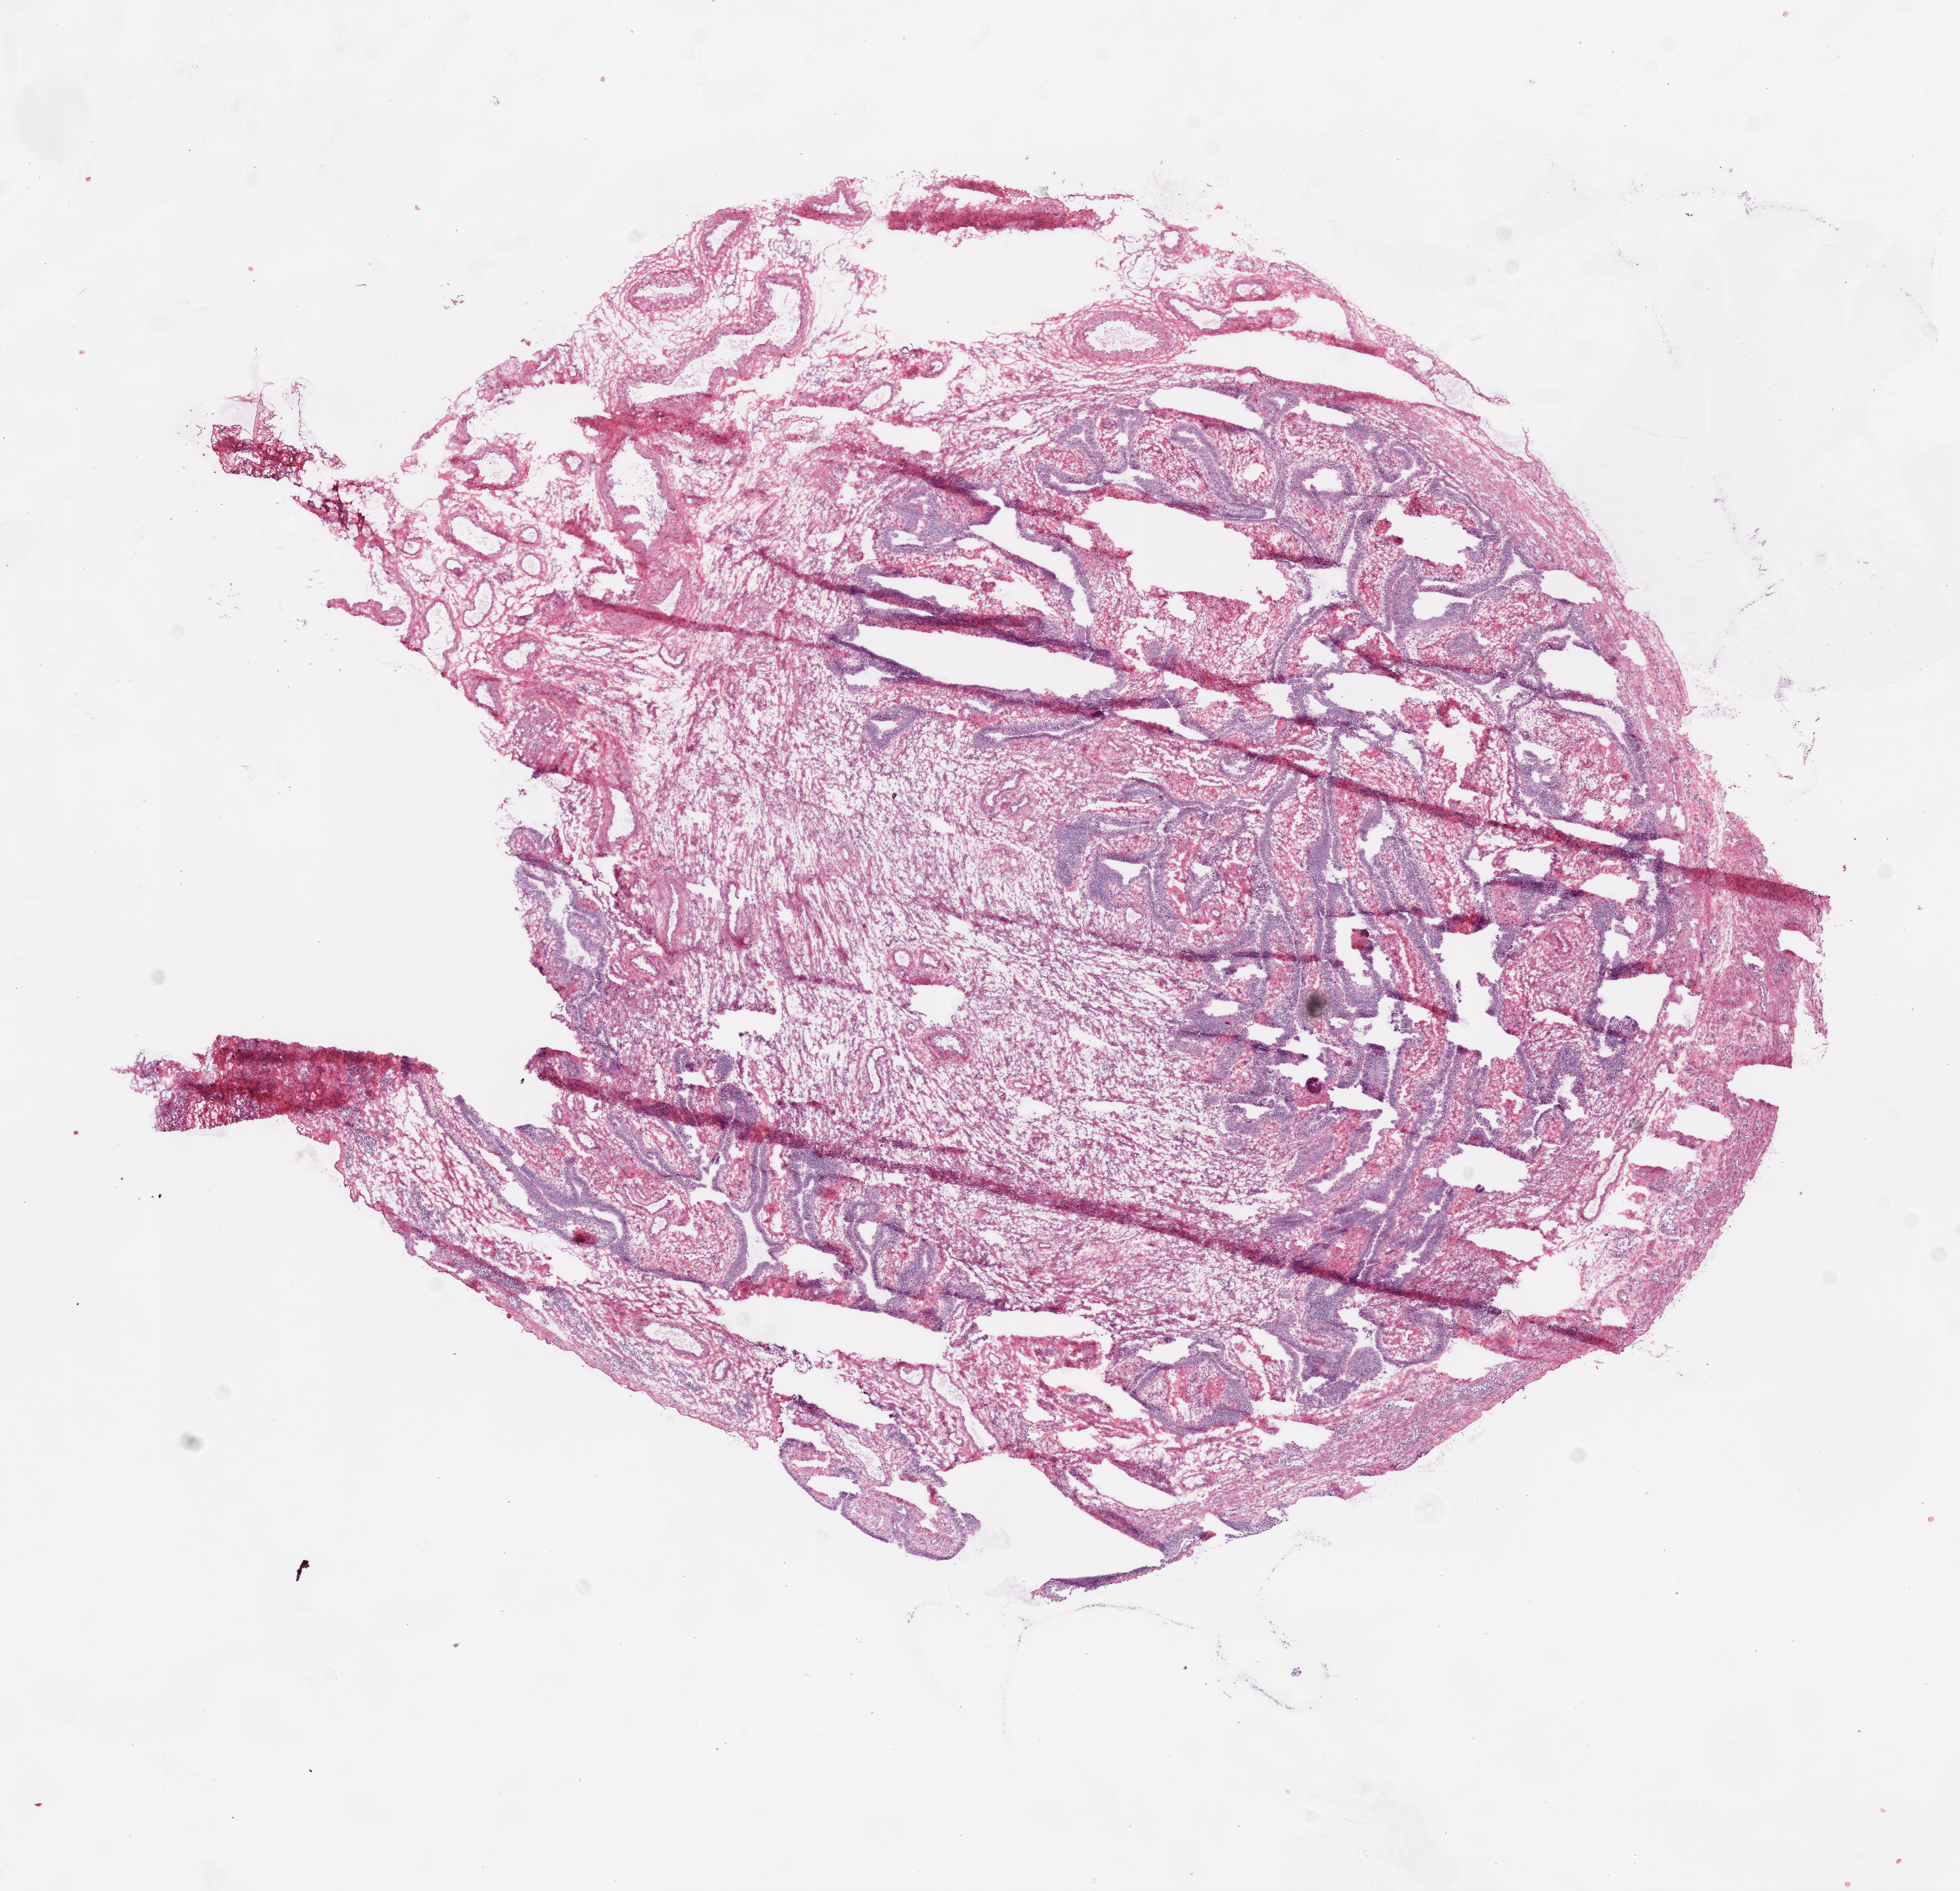
Whole-slide histology image, H&E-stained — low-resolution overview of the scanned area, about 12.0 x 11.6 mm (acquisition: 20x scan). Frozen section from the bottom of the tissue portion. Solid tissue normal (non-tumour tissue) sample from the ovary. Patient: female, age at initial diagnosis 52 years.
- this section: solid tissue normal sample (biorepository sample class)
- patient diagnosis: Serous cystadenocarcinoma, NOS